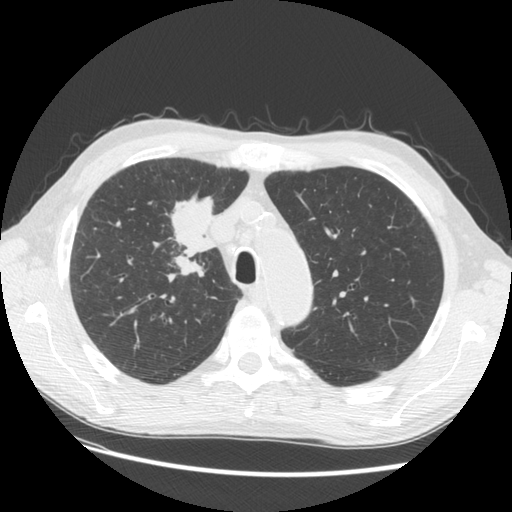
Chest CT (low-dose screening protocol), one axial image. Third screening round (two years after baseline). Lung window (W 1500 / L -600 HU). 2.5 mm slice thickness. Standard (soft-tissue) reconstruction kernel (STANDARD). Slice 33 of 133 in the series. 512 × 512 image matrix. Male participant, aged 73 years at enrolment. Current smoker at enrolment.
Lesion marked by an expert reader, bounding box <142,182,232,279> (left, top, right, bottom; pixels). The screening reader recorded 4 non-calcified nodules or masses ≥4 mm on this exam (right upper lobe, right upper lobe, right upper lobe, left lower lobe); which of them this box marks is not recorded. Lung cancer was diagnosed 48 days after this screen: squamous cell carcinoma, NOS, right upper lobe, poorly differentiated (G3), stage IIIB (AJCC 6th edition), 56 mm at pathology.